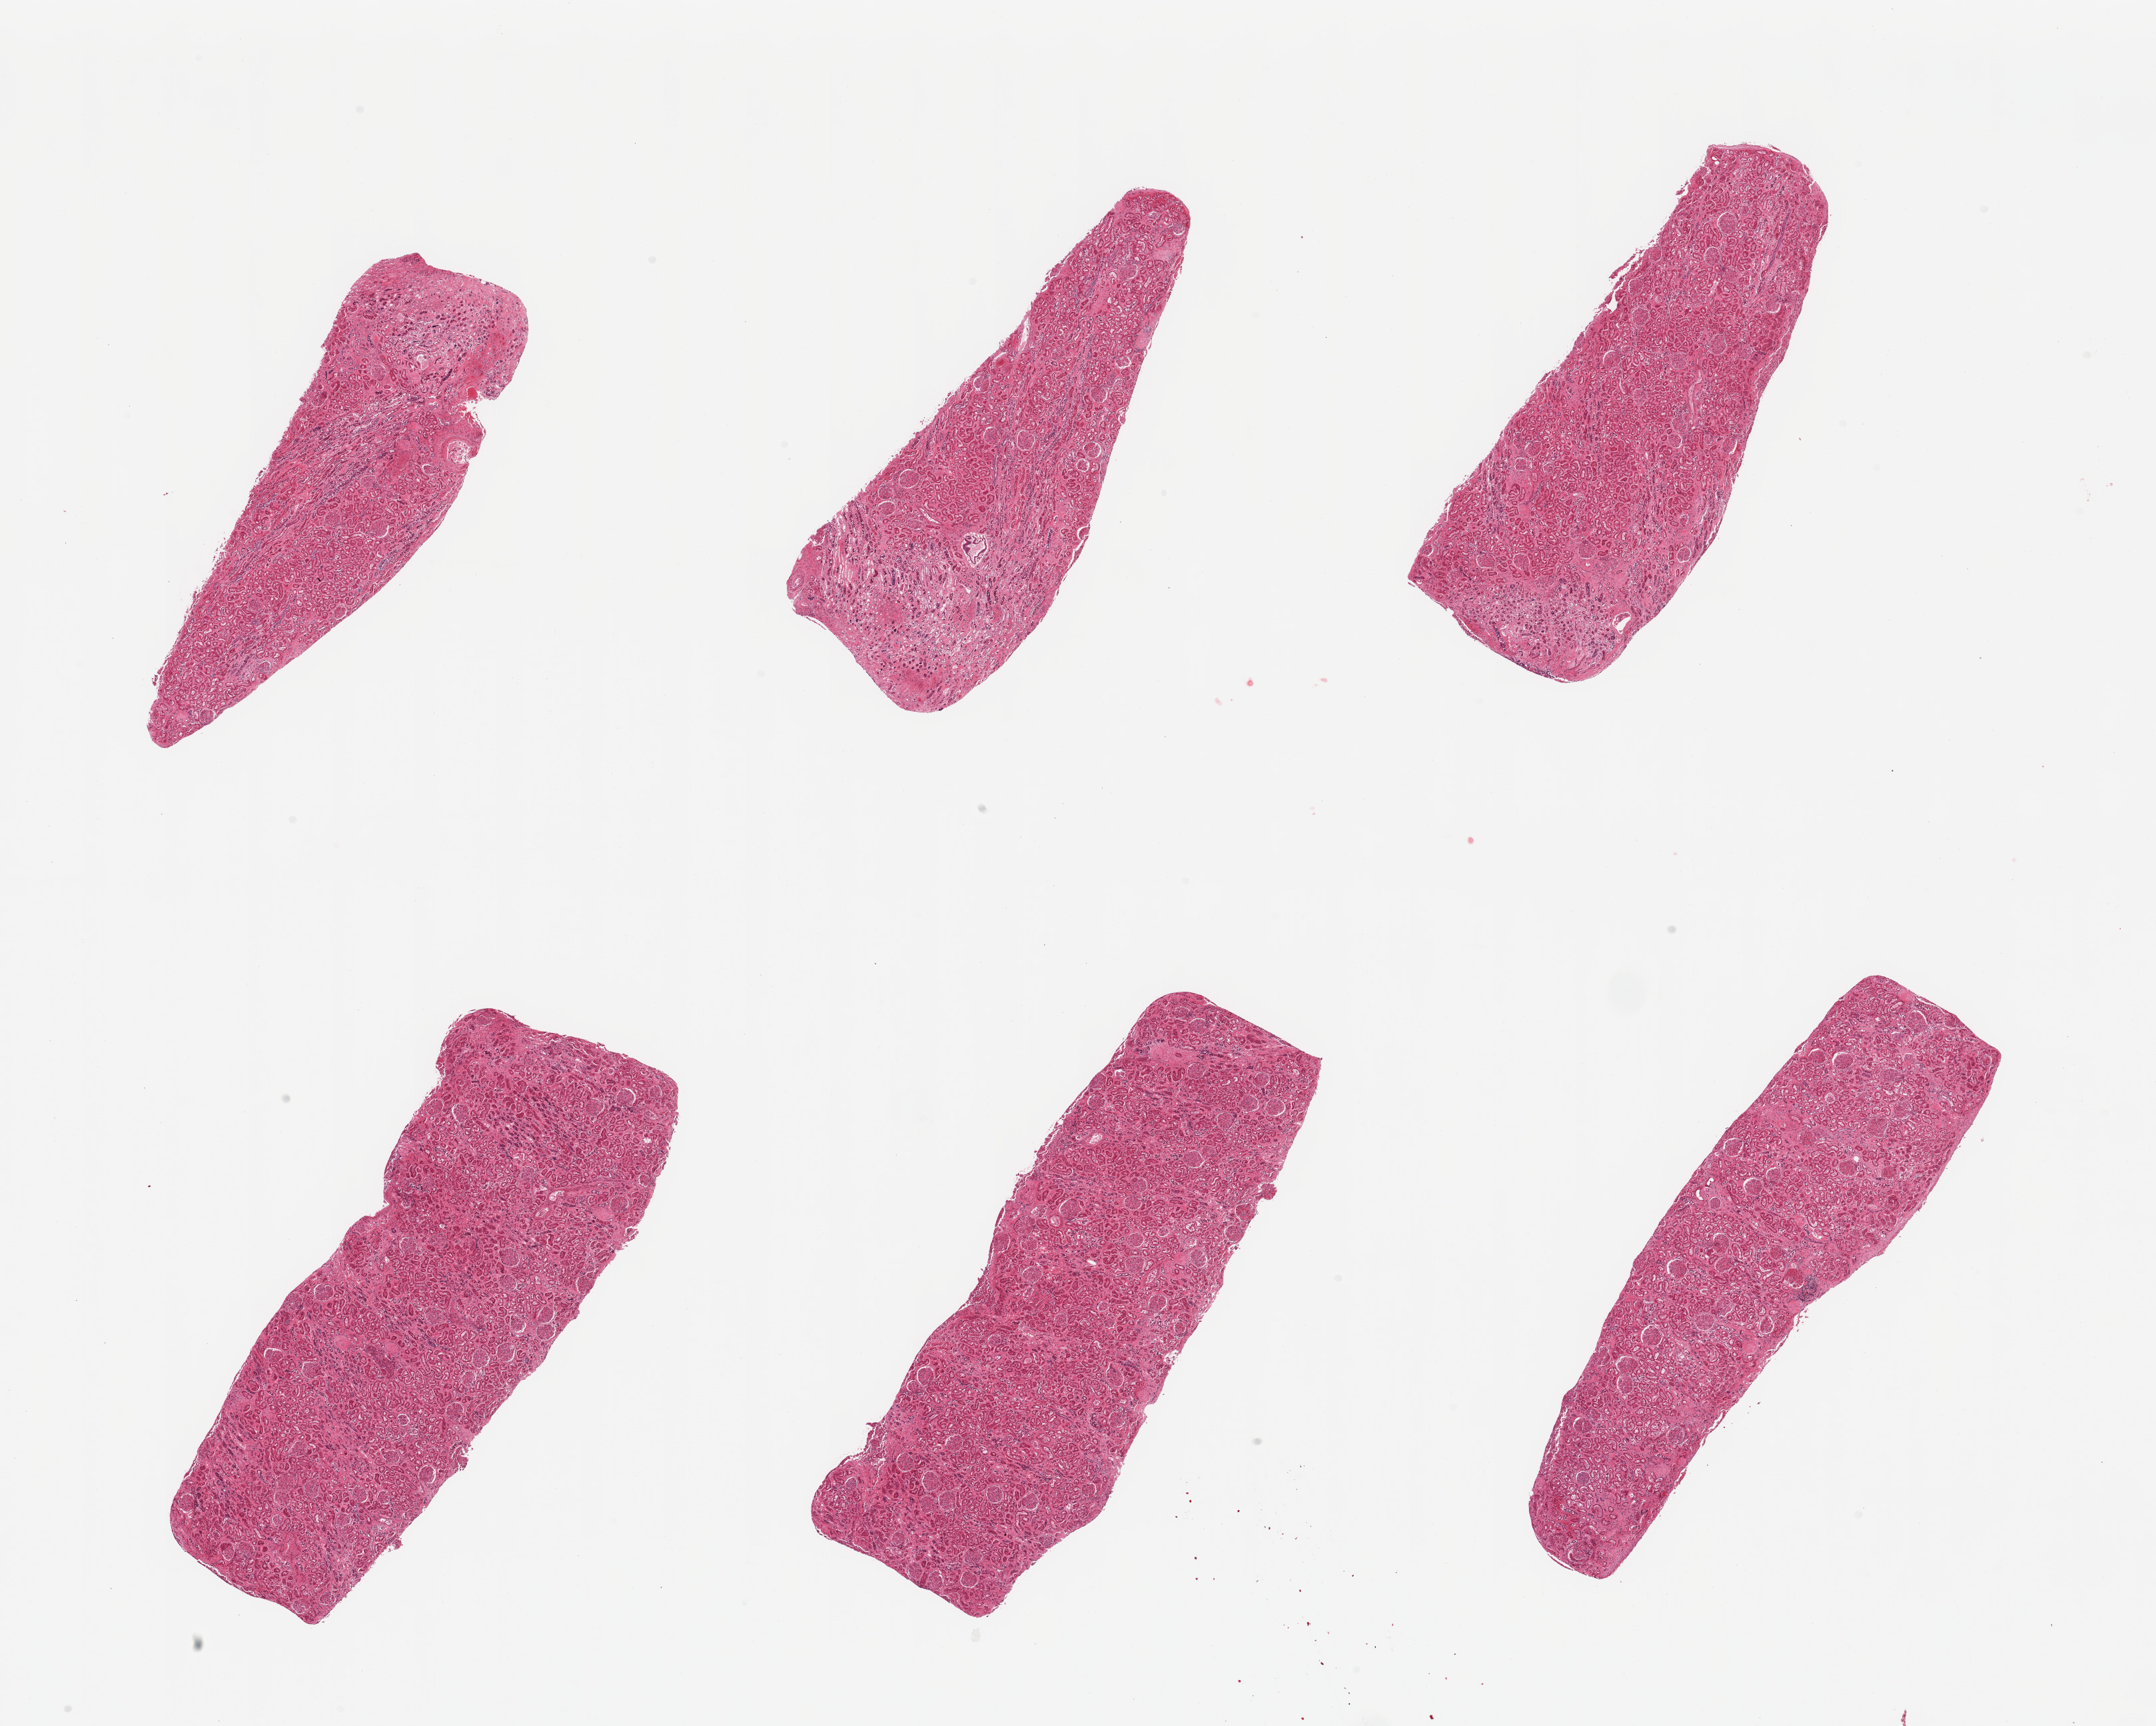
Digitized hematoxylin and eosin (H&E)-stained section, brightfield, a low-resolution overview of the entire scanned area, about 25.6 x 20.5 mm (acquisition: 20x scan). PAXgene-fixed, paraffin-embedded tissue. Target tissue: renal cortex. Tissue donor sample. Donor: male.
• pathologist's review note for this sample: 6 pieces; glomeruli in better shape than tubules